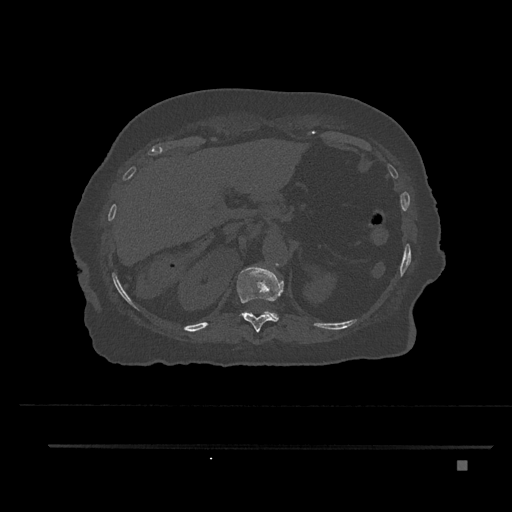
CT including the spine, one axial slice; slice 303 of 797 in the series (ordered by position); 120 kVp; bone window (W 1800 / L 400 HU); 0.5 mm slice thickness; 512 × 512 image matrix, field of view 437 × 437 mm. Patient: female, 76 years. Case-level facts recorded for this patient, not image findings: primary cancer: lung.
Annotated regions visible in this slice (semi-automatically segmented with operator editing):
- T11 vertebra: bounding box (x1, y1, x2, y2) in pixels: (237, 265, 284, 332)
- T12 vertebra: (262, 311, 279, 320)